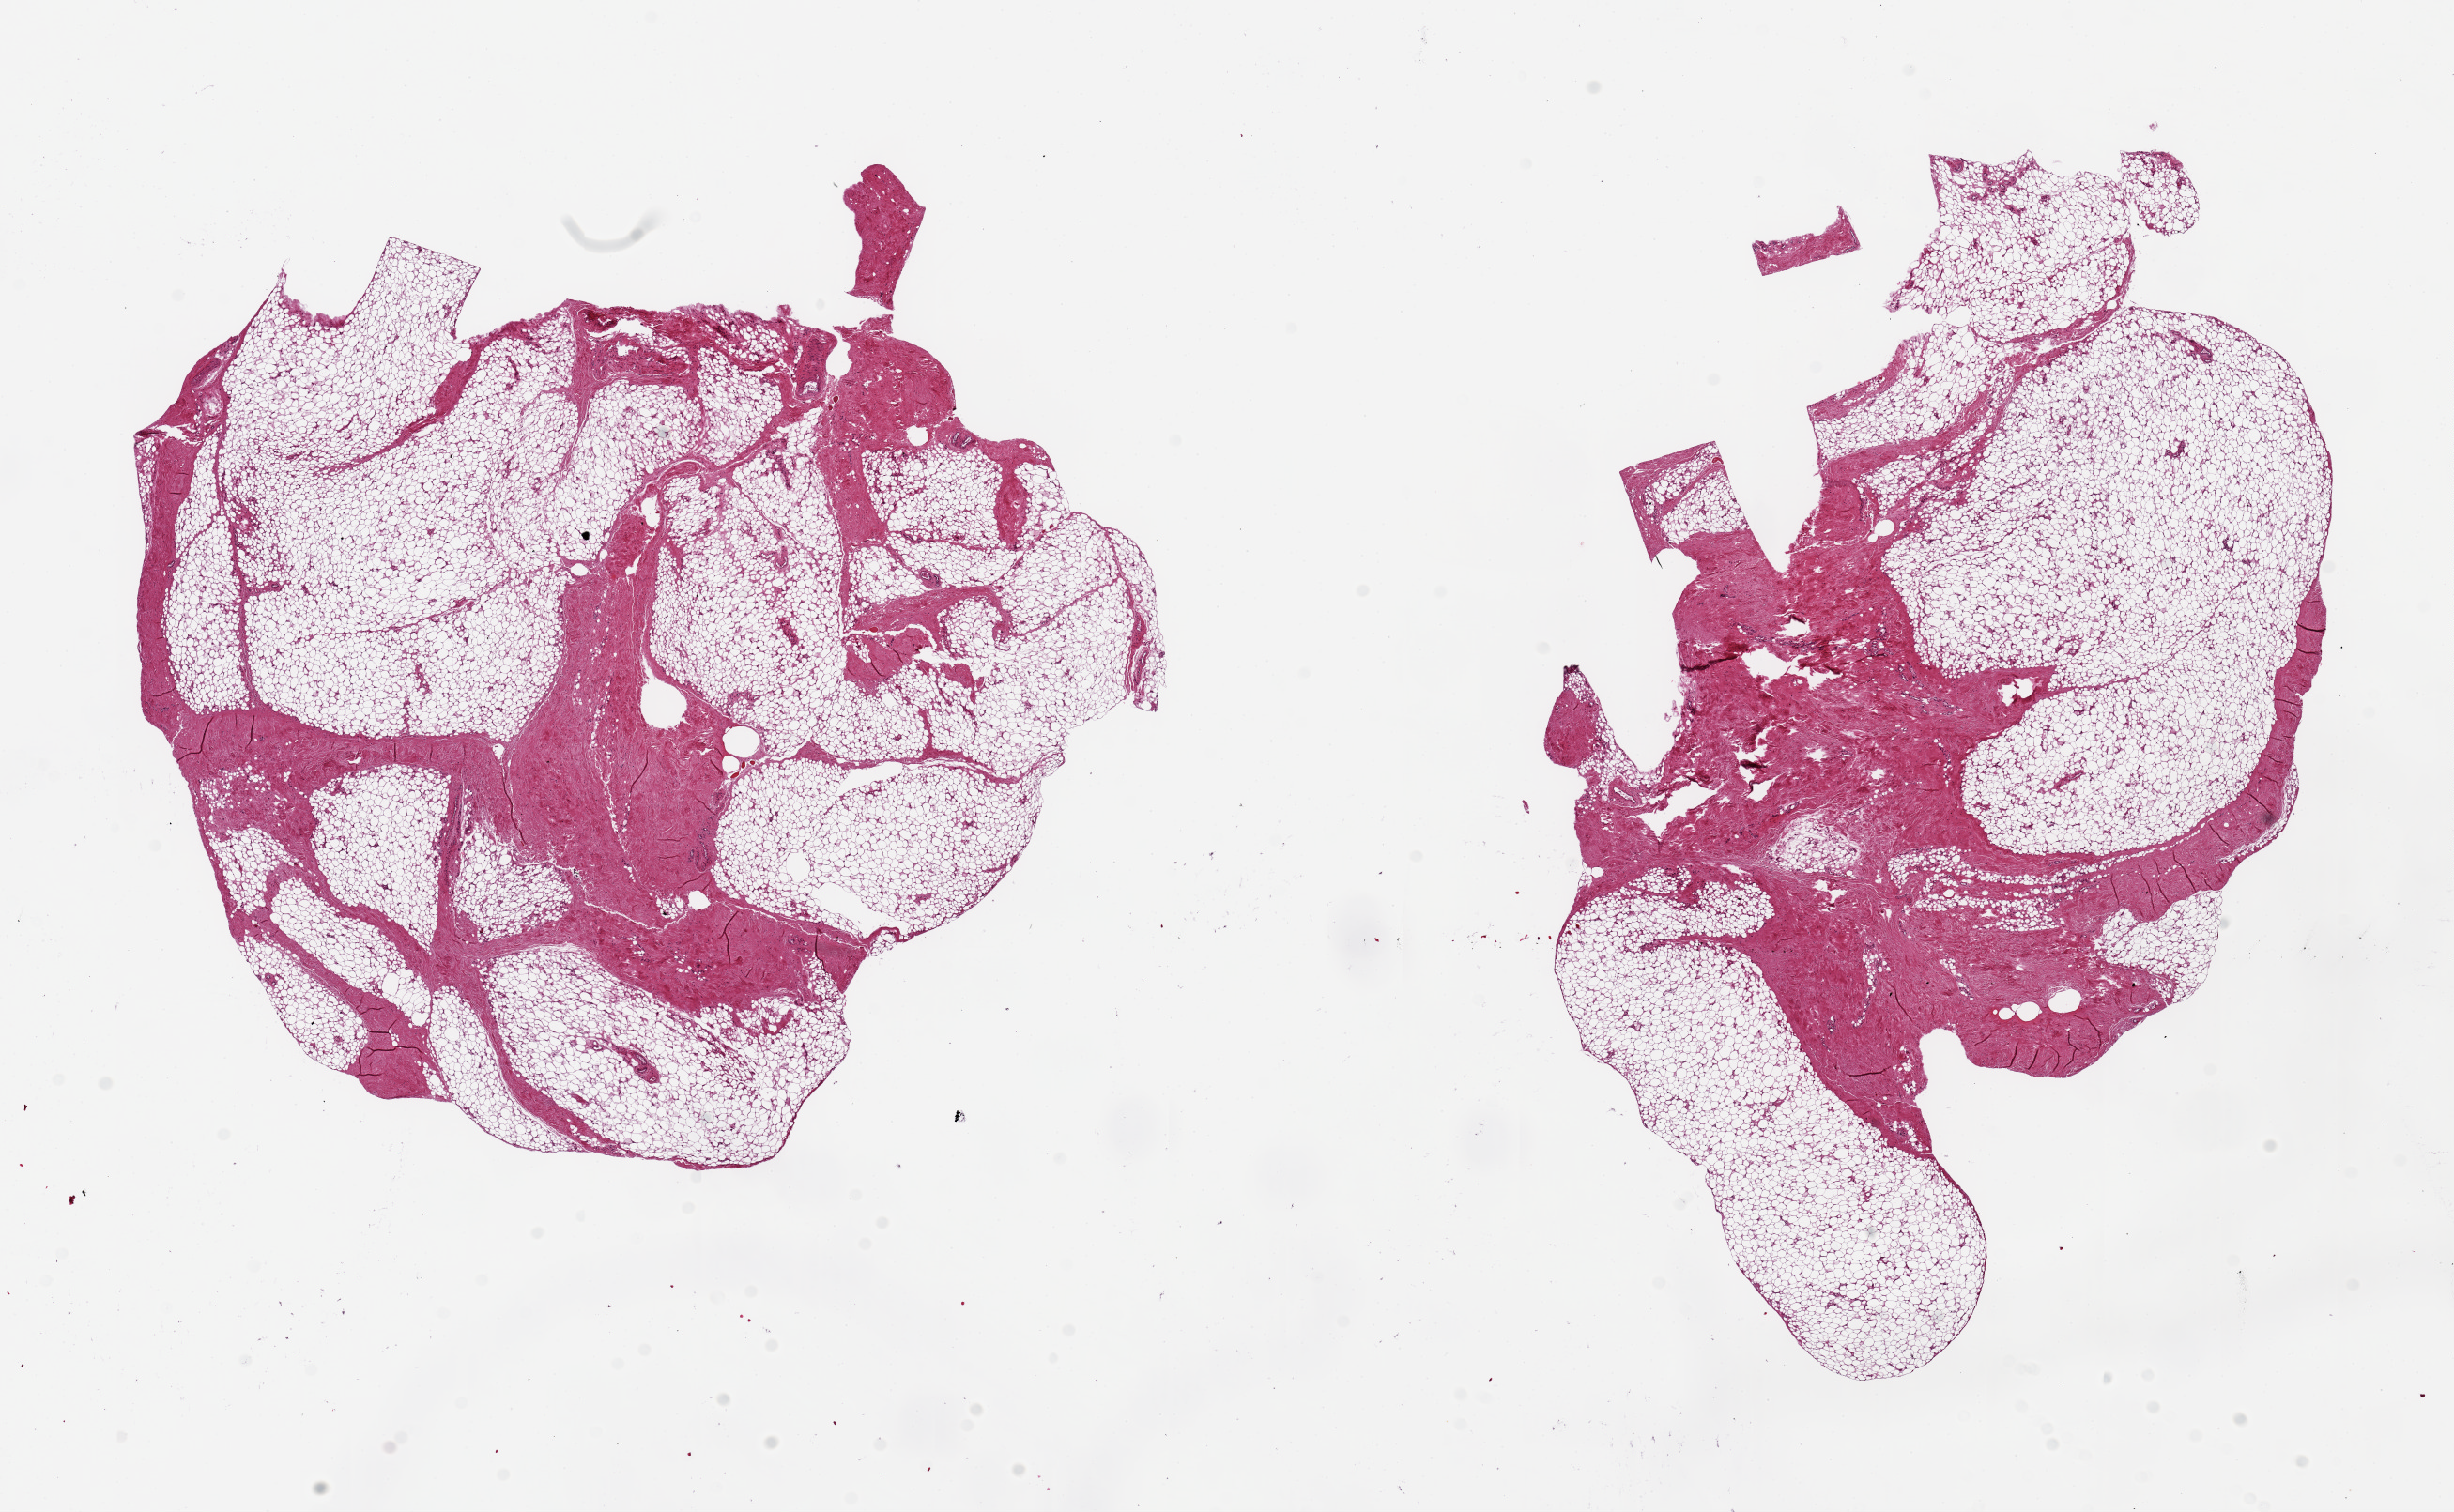
Digitized haematoxylin and eosin-stained section, shown as a low-resolution overview of the whole scanned area (about 20.7 x 12.7 mm); PAXgene-fixed paraffin-embedded (PFPE) section; target tissue: breast; donor tissue sample. Donor sex: male.
• reviewer comment on this tissue sample: 2 pieces, 9x9 & 10x7mm; Fibroadipose tissue without ducts